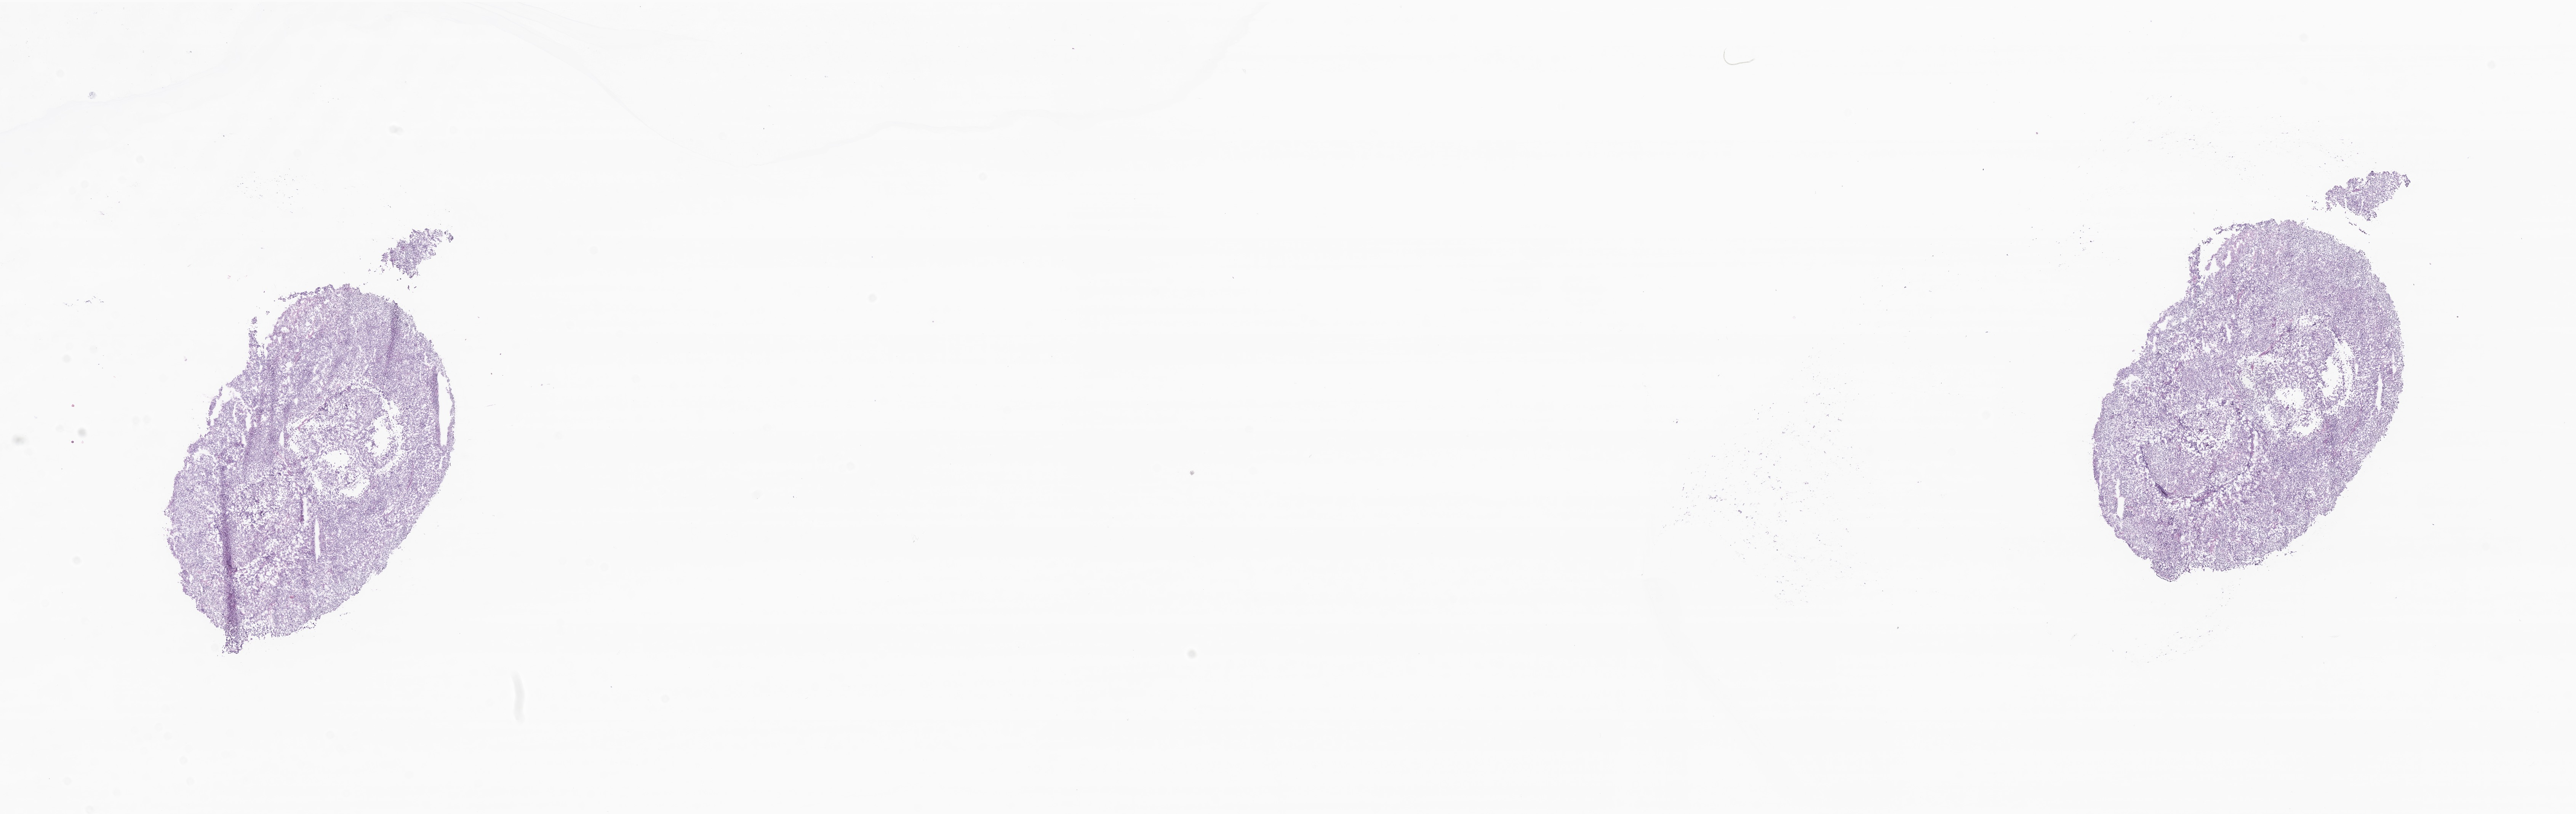
H&E whole-slide image of tumor tissue from the brain stem, whole scanned area (about 28.5 x 9.0 mm) shown as a low-resolution overview, cryosection (OCT / tissue freezing medium). Patient male; age 74 months (6 years 2 months).
• recorded diagnosis: Medulloblastoma, NOS